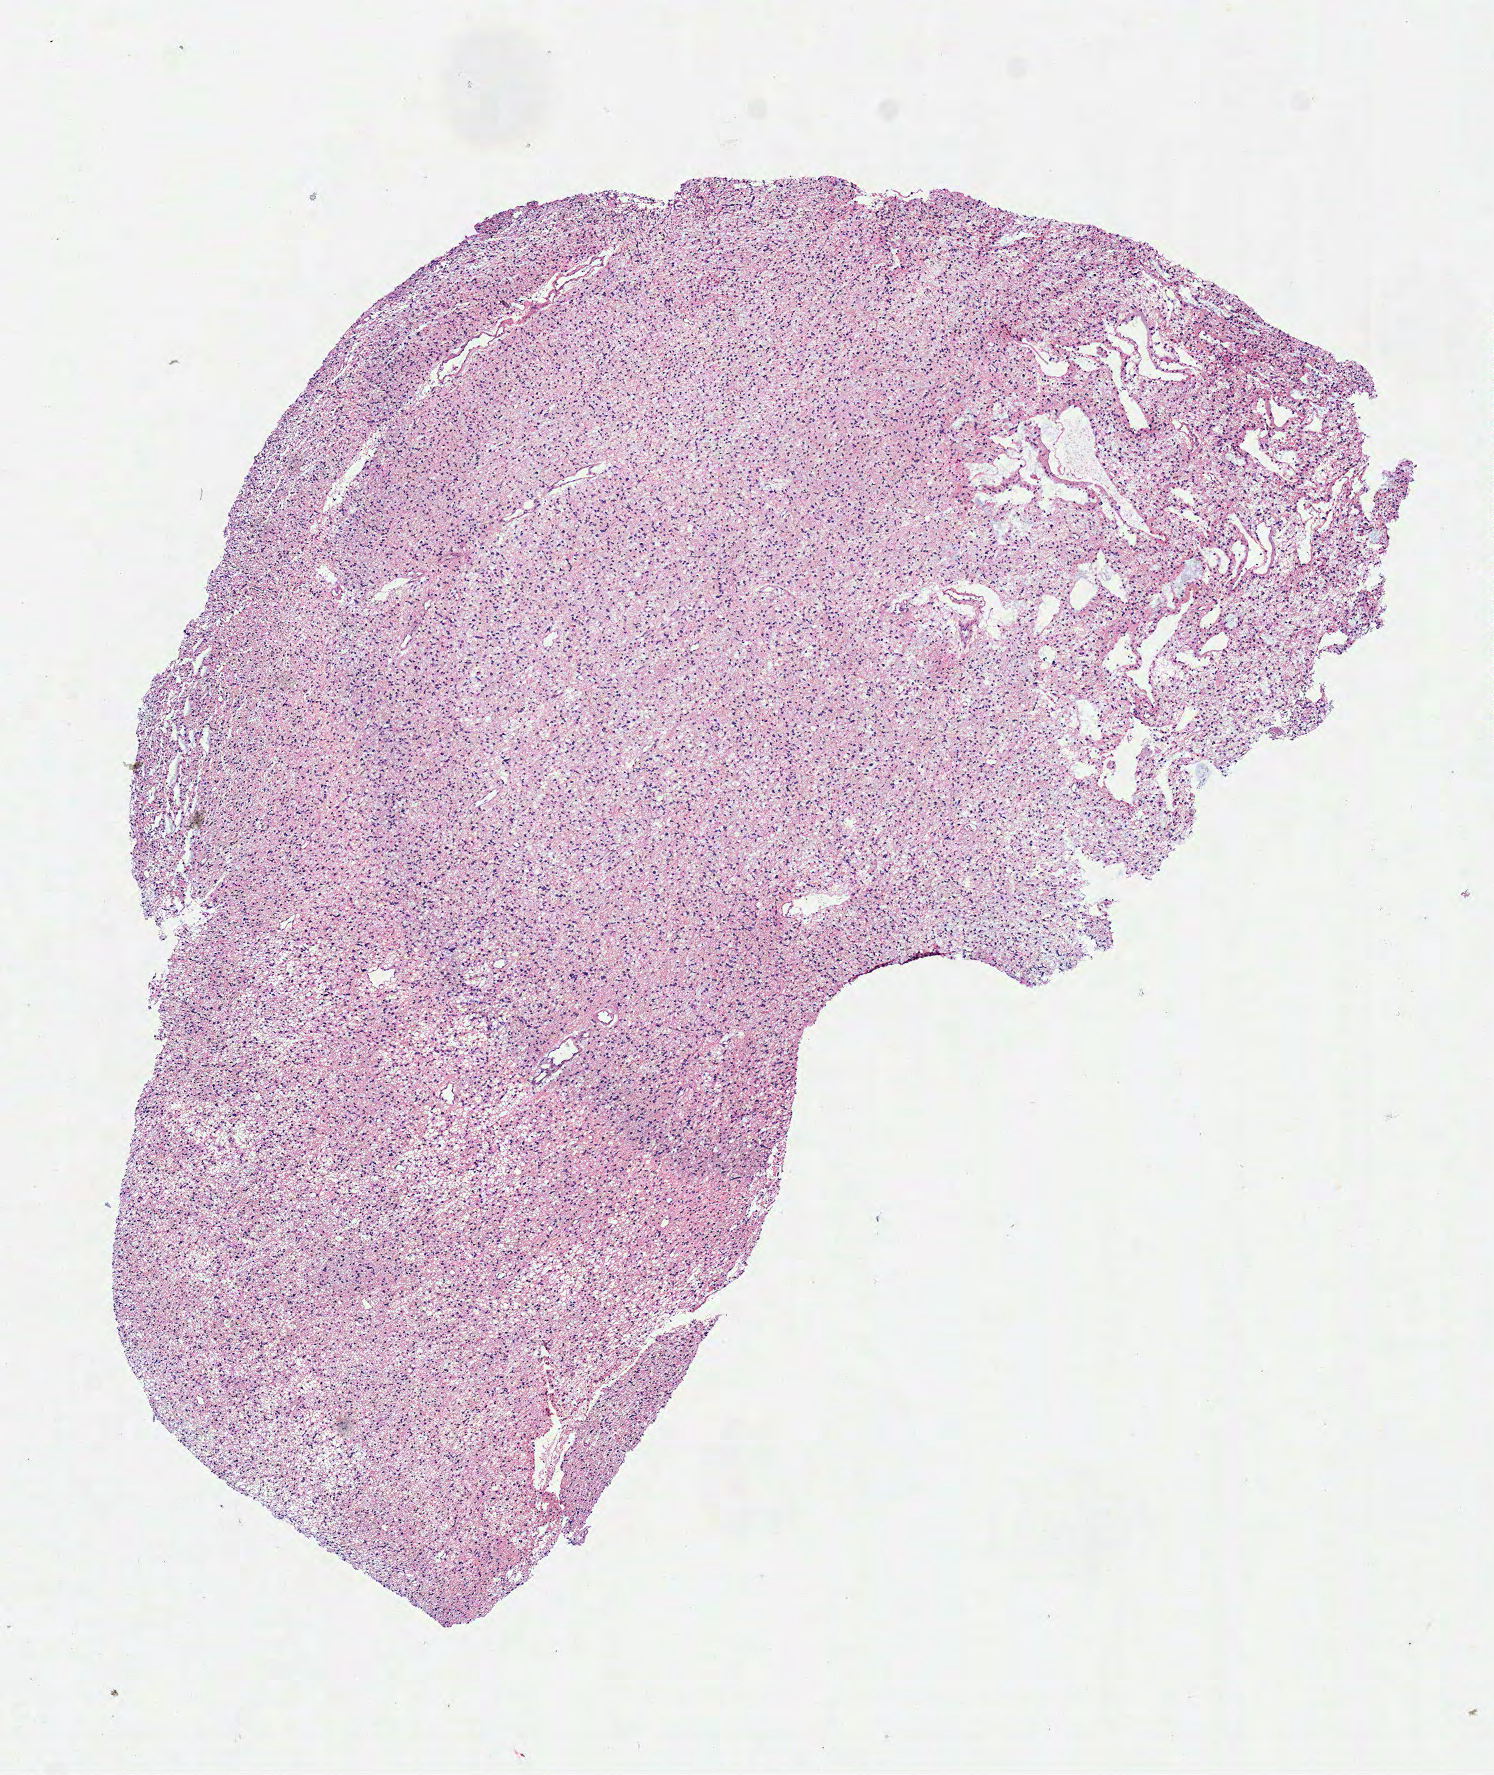
Whole-slide histology image, Hematoxylin and eosin (H&E) stained, a low-resolution overview of the entire scanned area, about 5.9 x 7.0 mm. Frozen section from the top of the tissue portion. Primary tumour sample from the brain. Female, age 35 years at initial diagnosis. Histologic grade: G2 (moderately differentiated). Composition of this section per pathologist review: tumour cells 100%, tumour nuclei 75%, normal cells 0%, stromal cells 0%, necrosis 0%.
• histologic diagnosis: Oligodendroglioma, NOS (cerebrum)